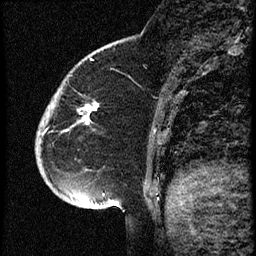
Breast MRI (dynamic contrast-enhanced), one sagittal slice; position 14 of 60 along the scan axis; dynamic contrast-enhanced study with each time point stored as its own series, time point 2 of 3 at this slice position (early post-contrast, ordered by acquisition time); 1.5 T; TE 4.2 ms, TR 18.9 ms; 2 mm slice thickness; 256 × 256 image matrix, field of view 200 × 200 mm. Female patient. From the clinical record (not read from this slice): setting: breast cancer imaged before/during neoadjuvant chemotherapy; receptor status: HR-positive, HER2-negative.
Outlined on this slice (semi-automatic segmentation, software-assisted and operator-edited):
- analysis volume of interest (the breast-tissue region the enhancement analysis was run in; not a lesion): bounding box (x1, y1, x2, y2) in pixels: (36, 87, 102, 173)
- tumour enhancement mask (voxels above the 100 % enhancement threshold inside the analysis volume of interest): (88, 104, 98, 114)